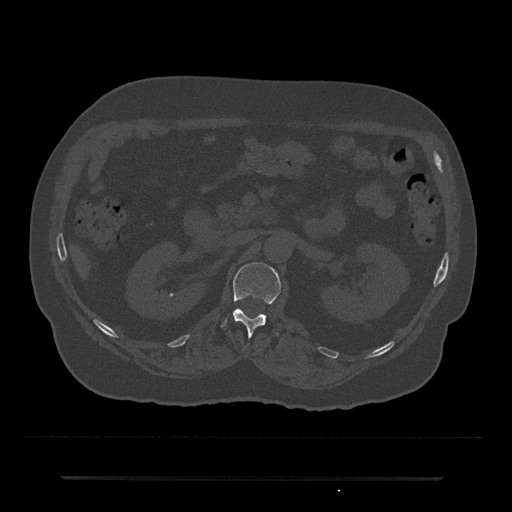
CT including the spine, one axial slice. Slice 67 of 797 in the series (ordered by position). Reconstruction kernel Br40s/3. 120 kVp. Bone window (W 1800 / L 400 HU). 0.5 mm slice thickness. 512 × 512 image matrix, field of view 437 × 437 mm. Male patient, age 69 years. From the clinical record (not read from this slice): primary cancer: prostate.
Structures marked on this image (semi-automatic segmentation, software-assisted and operator-edited):
- L1 vertebra: bounding box (x1, y1, x2, y2) in pixels: (221, 262, 281, 337)